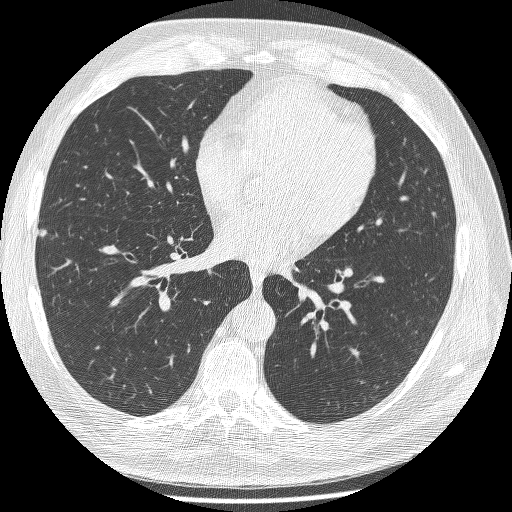
Low-dose screening chest CT, one axial slice; slice 109 of 241 in the series (ordered by position); reconstruction kernel BONE; lung window (W 1500 / L -600 HU); 1.25 mm slice thickness; 512 × 512 image matrix, field of view 346 × 346 mm.
Annotated regions visible in this slice (expert manual segmentation):
- lesion 1 (tumor, lower lobe of right lung): bounding box [x1, y1, x2, y2] px = [39, 229, 48, 237]